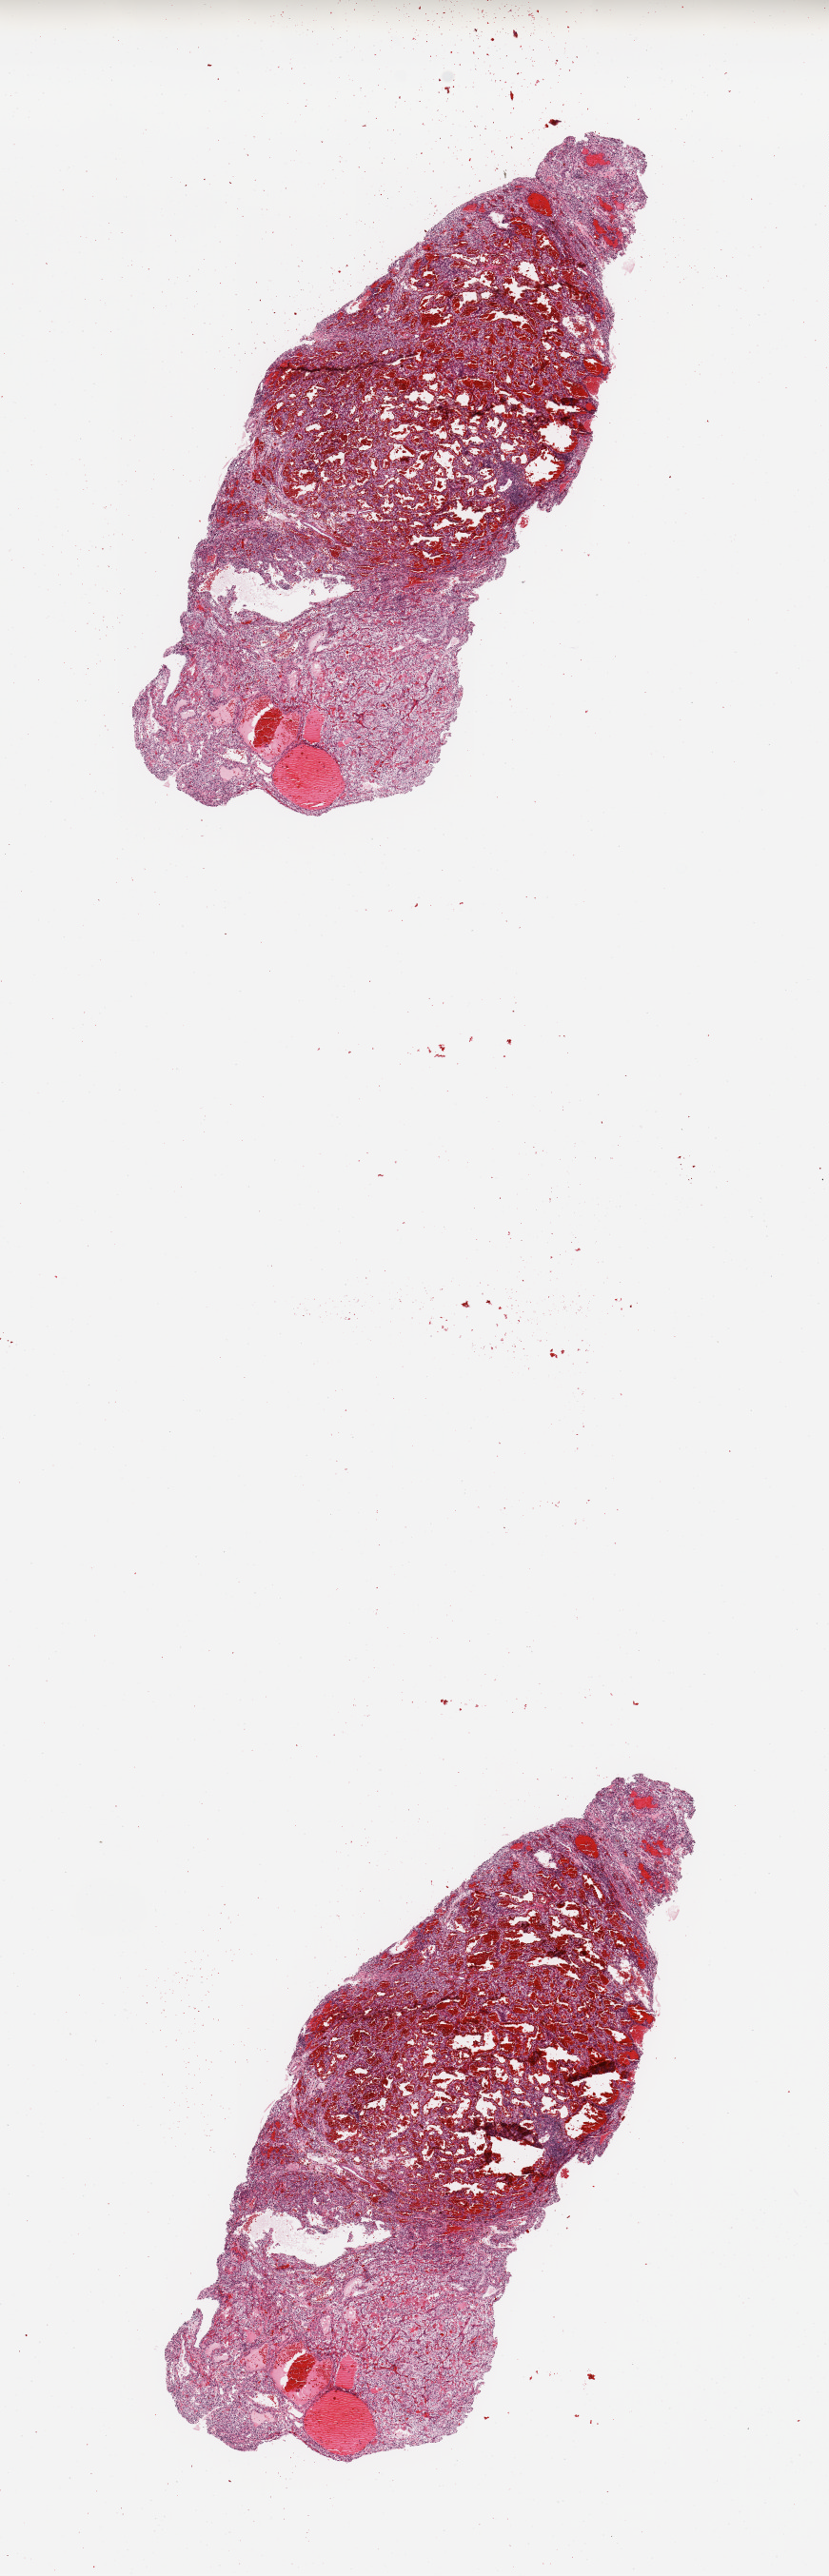
Whole-slide histology image, H&E, a low-resolution overview of the entire scanned area, about 6.9 x 21.4 mm (from a 20x scan), tumour tissue sample, sampled site: kidney. Patient: male, age 37 years. Histologic grade: G3 (poorly differentiated). Composition of this section per pathologist review: tumour nuclei 90%, necrosis 5%.
• primary tumour site (as recorded): middle
• AJCC pathologic stage: I
• diagnosis: Renal cell carcinoma, NOS